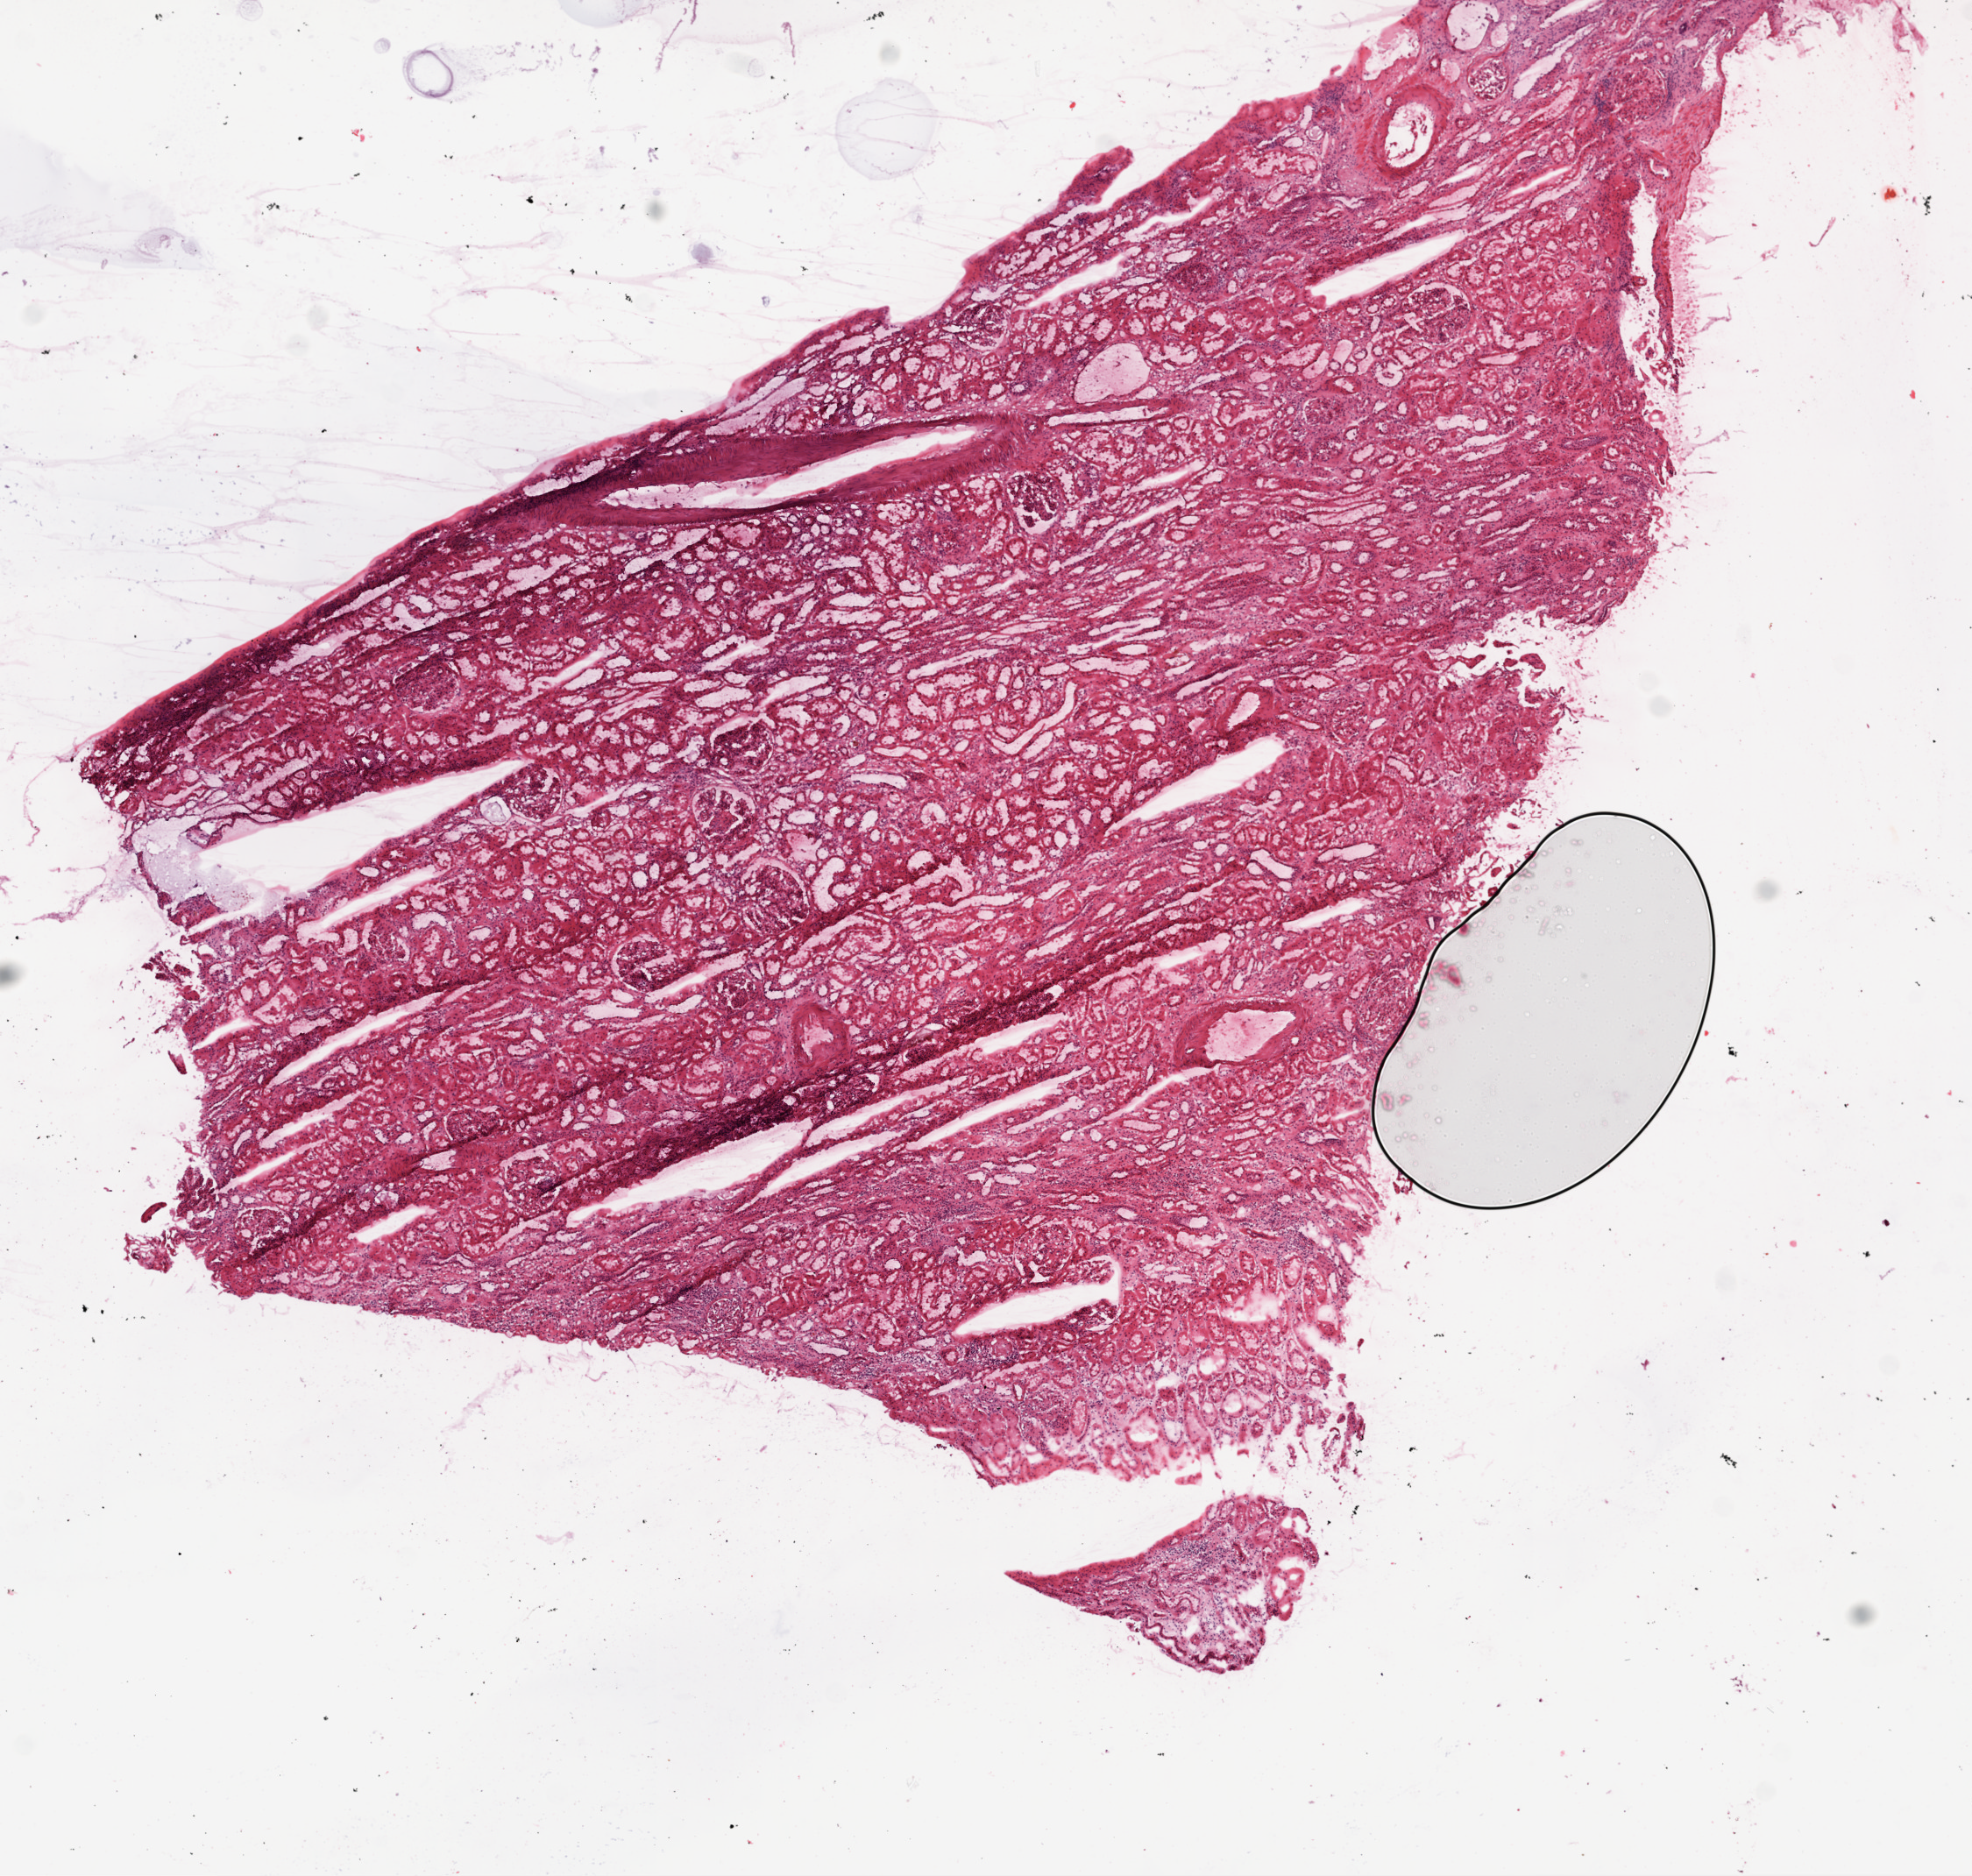
Digitized Hematoxylin and eosin (H&E) stained tissue section (whole slide) — a low-resolution overview of the entire scanned area, about 9.0 x 8.6 mm. Frozen section from the top of the tissue portion. Solid tissue normal (non-tumour tissue) sample from the kidney. Male, age 54 years at initial diagnosis.
This section: solid tissue normal sample (biorepository sample class). Patient diagnosis: Clear cell adenocarcinoma, NOS.